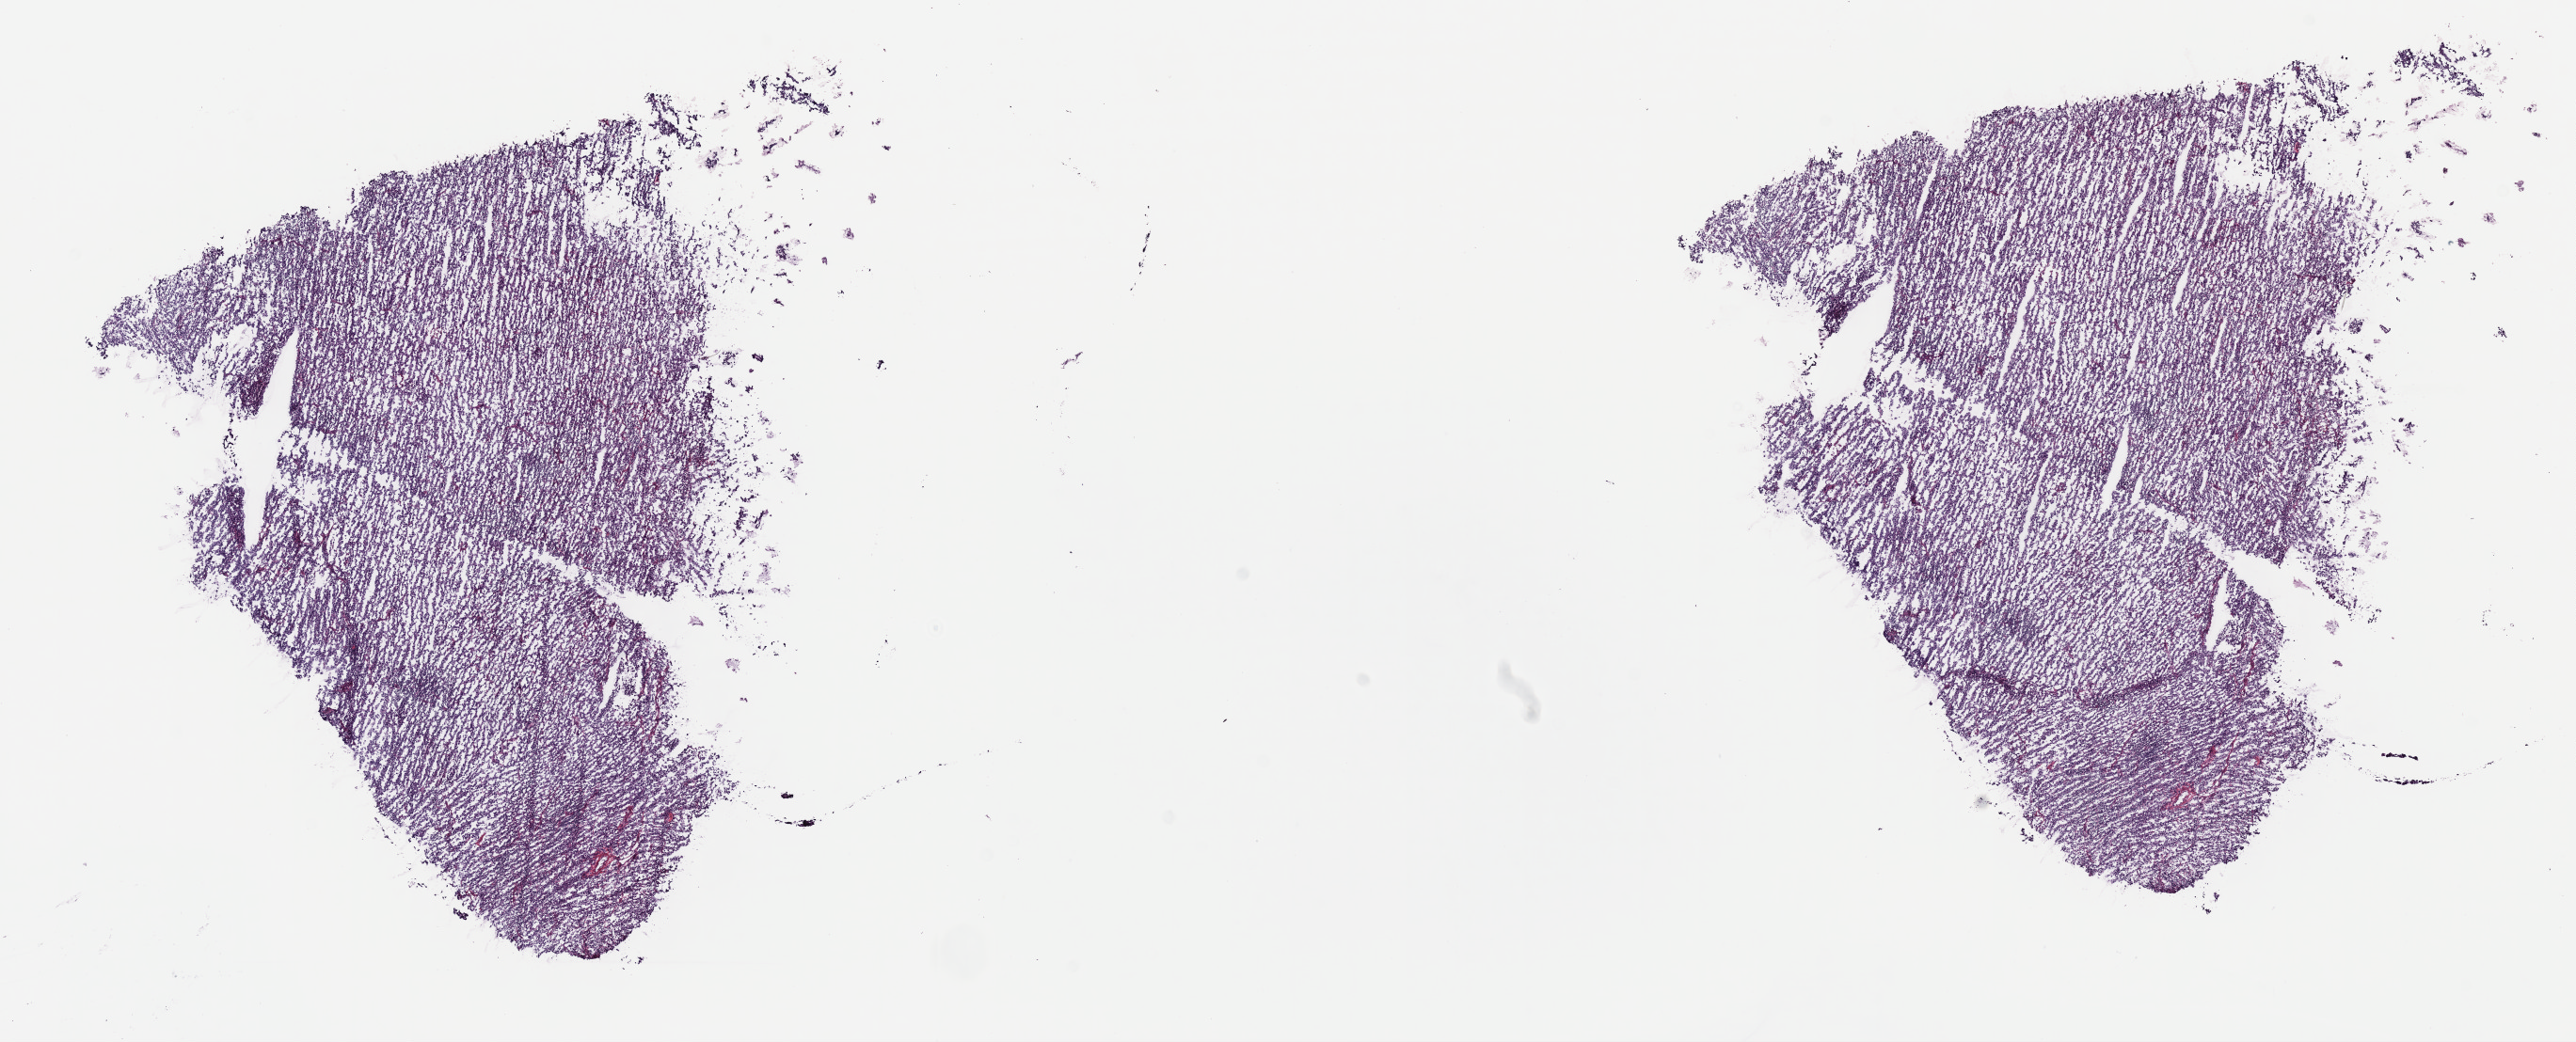
Digitized H&E tissue section (whole slide), low-resolution overview of the scanned area, about 22.1 x 9.0 mm. Frozen section from the top of the tissue portion. Sample: primary tumour, testis. Male patient; age at initial diagnosis 50 years. Composition of this section per pathologist review: tumour cells 95%, tumour nuclei 95%, normal cells 0%, stromal cells 5%, necrosis 0%. Inflammatory infiltration, as recorded: lymphocyte infiltration 60%, monocyte infiltration 20%, neutrophil infiltration 10%.
• AJCC pathologic stage: IA (6th edition)
• histologic diagnosis: Seminoma, NOS